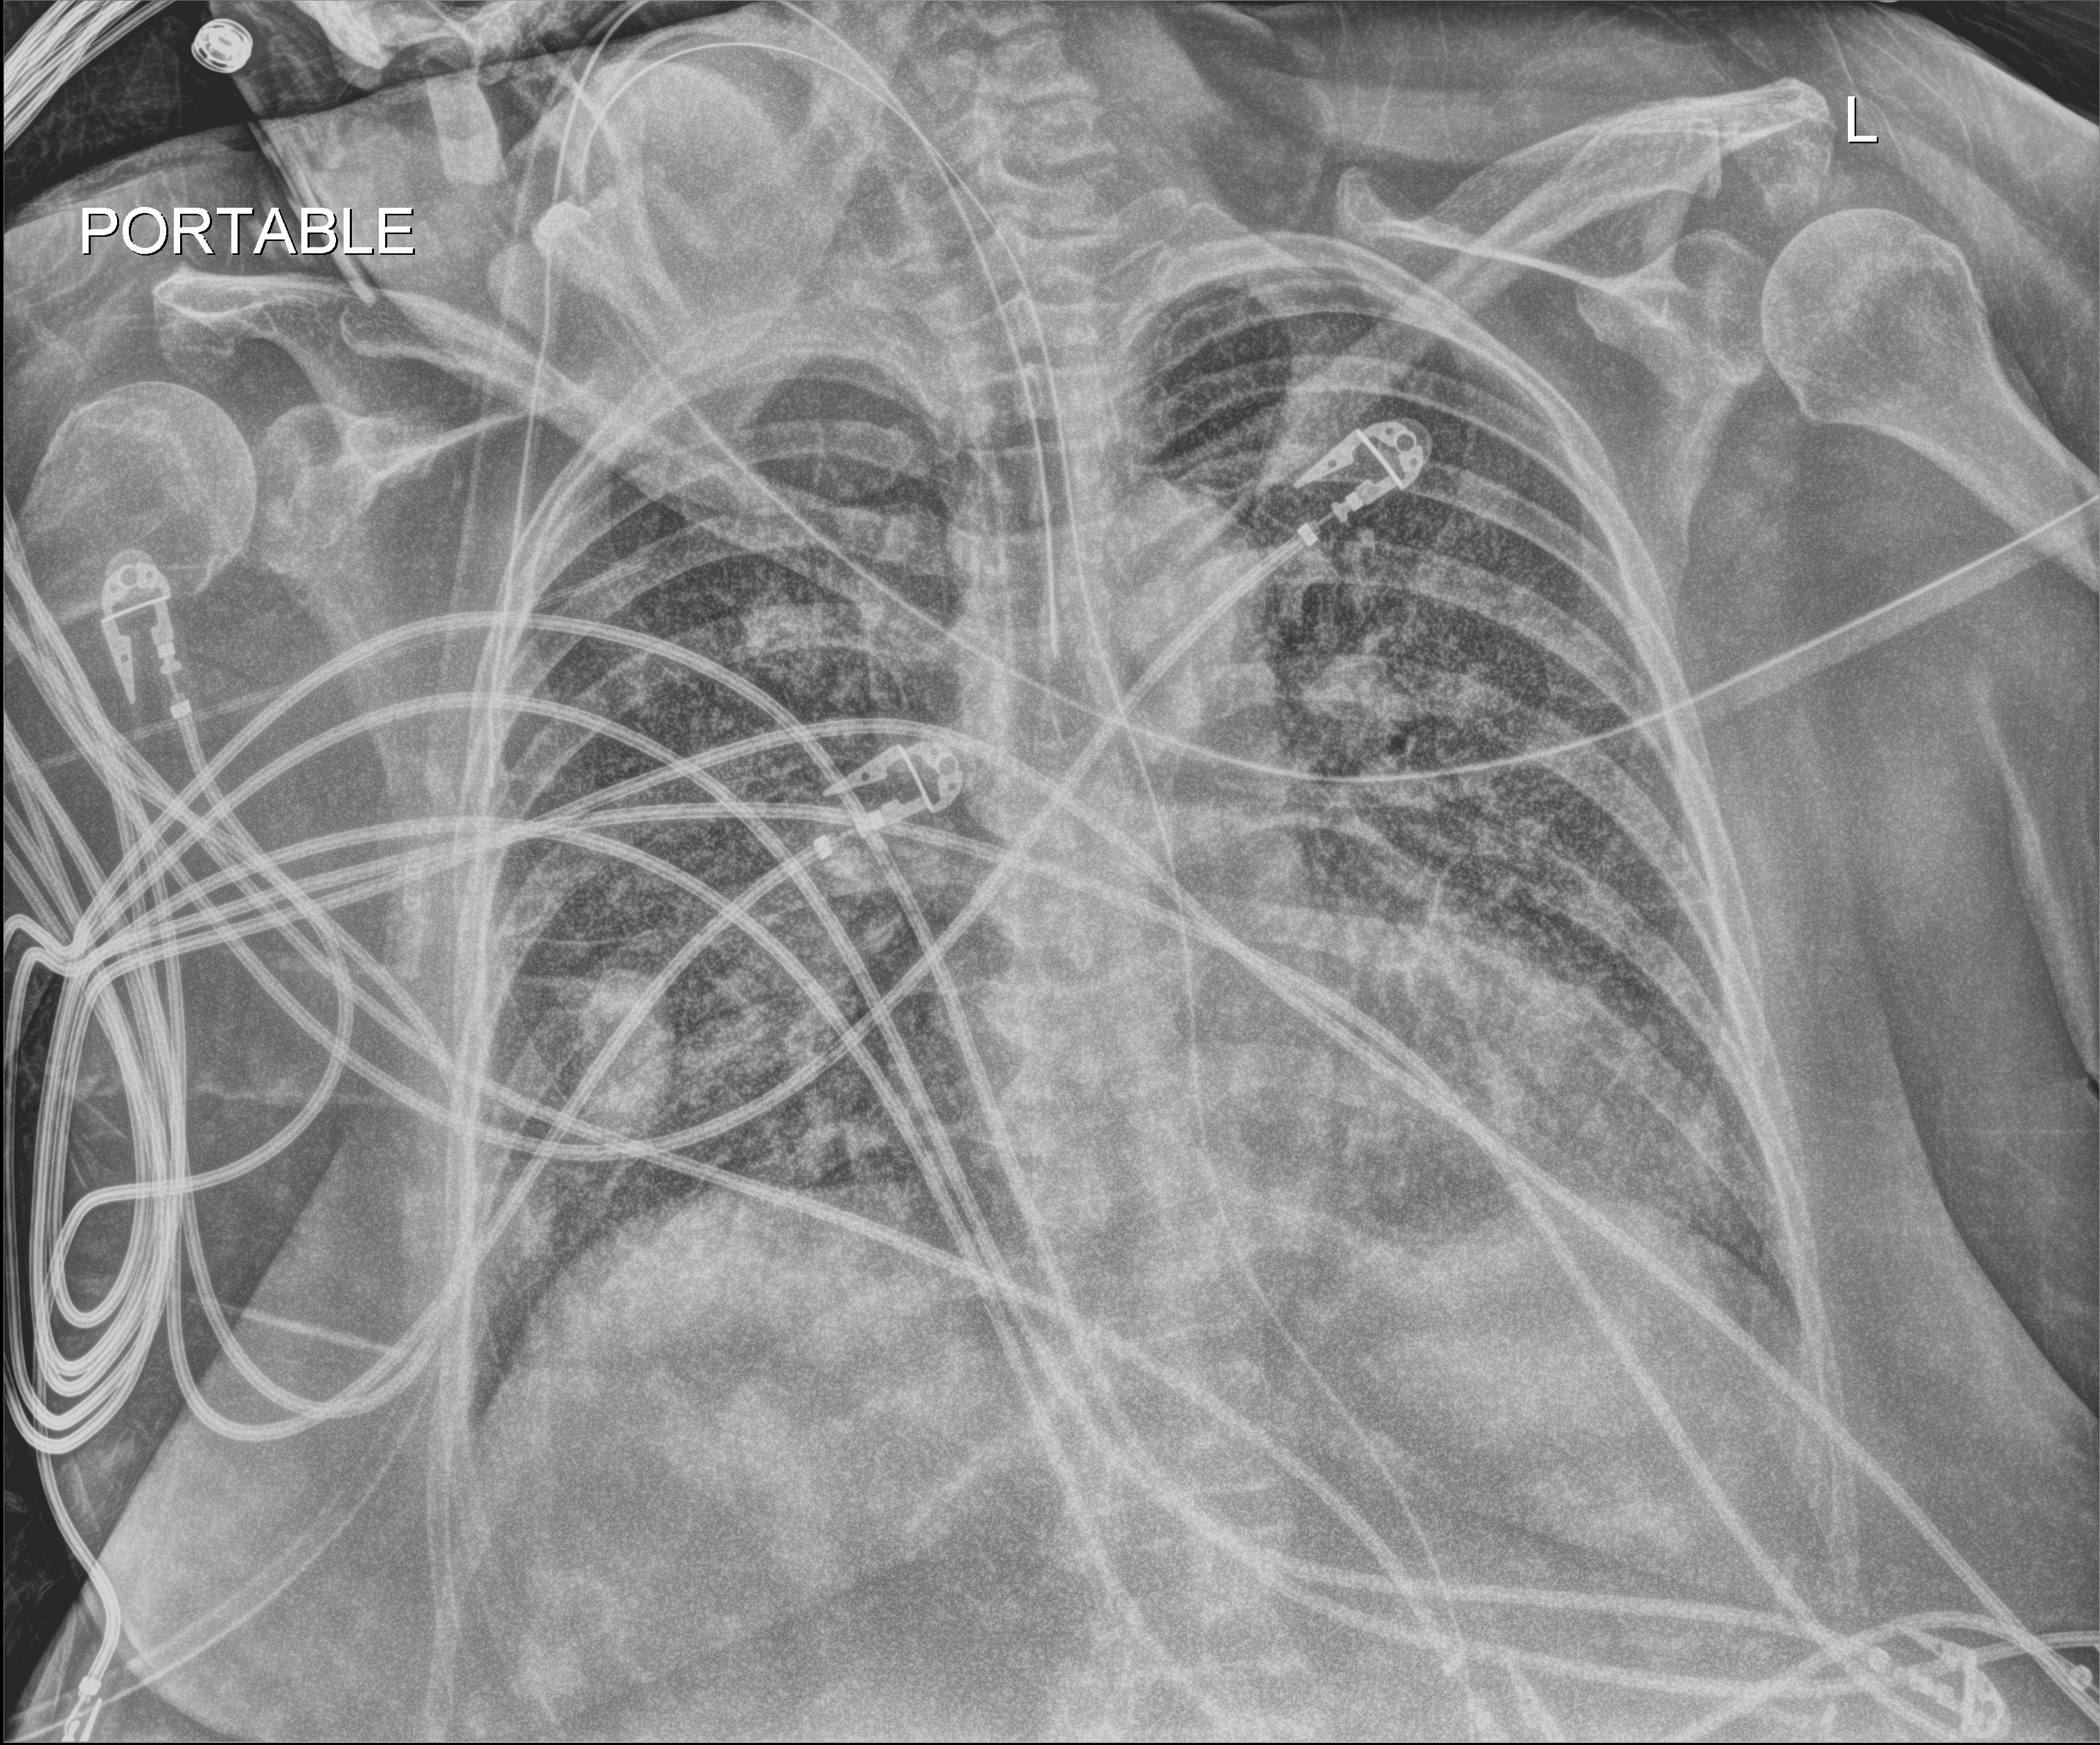
Chest radiograph, anteroposterior (AP) projection. Female patient hospitalised with COVID-19, age 60–74 years.
Hospital-stay facts (about this admission, not read from this image; timing relative to this image not recorded):
- admitted to intensive care during this hospital stay: yes
- smoking status (admission record): former